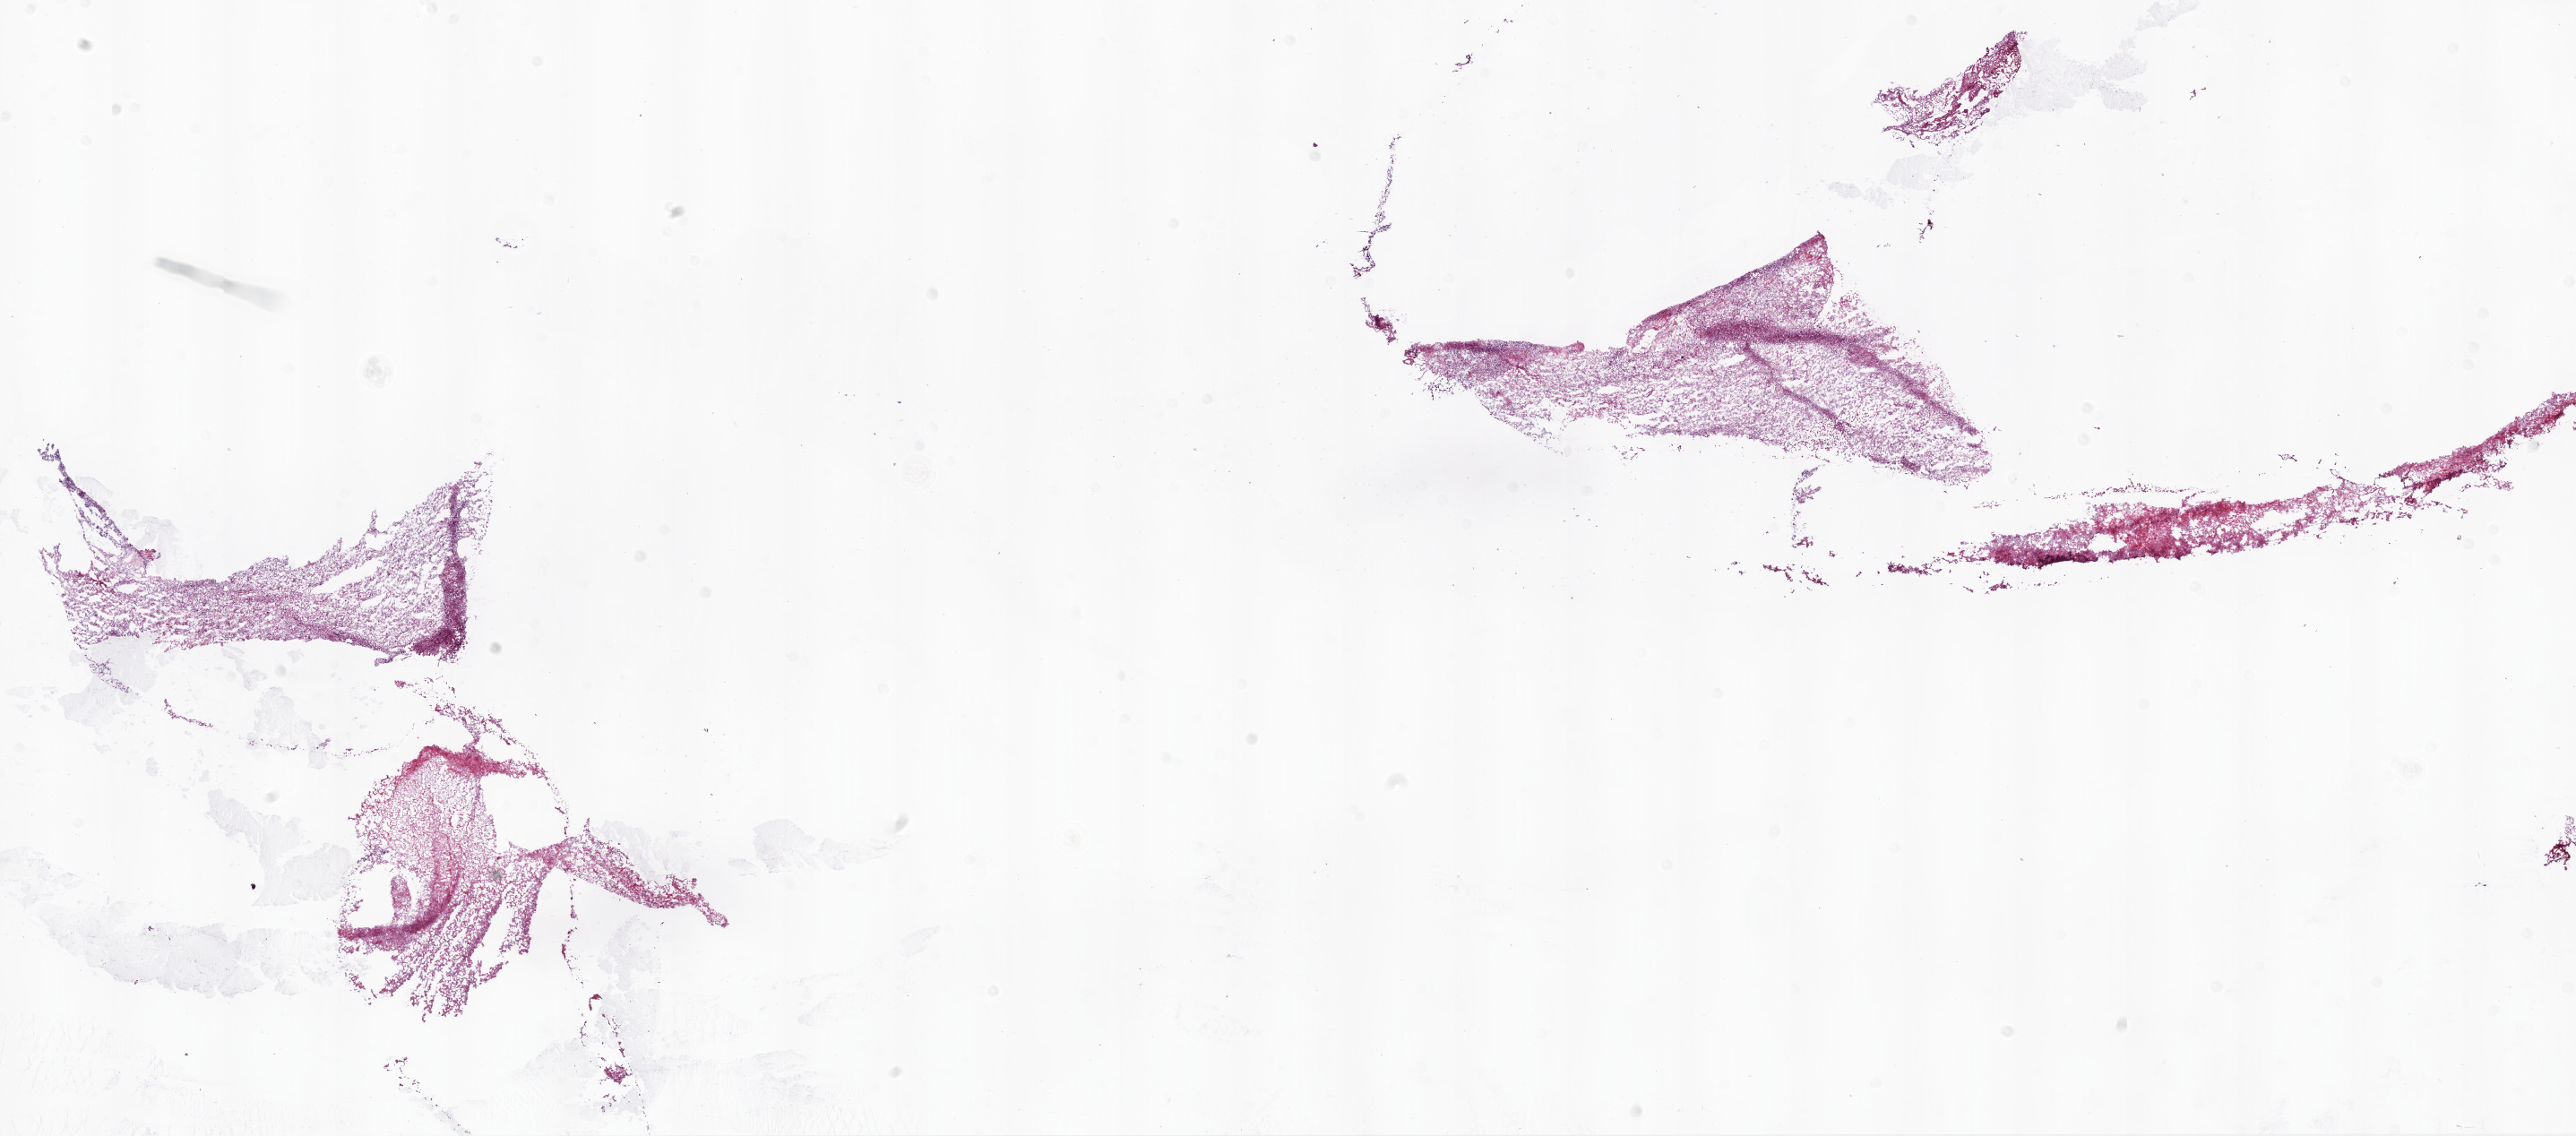
Whole-slide histology image, H&E-stained — a low-resolution overview of the entire scanned area, about 23.1 x 10.2 mm, frozen section from the bottom of the tissue portion, brain, primary tumour sample. Male, age 59 years at initial diagnosis. Composition of this section per pathologist review: tumour cells 95%, tumour nuclei 100%, normal cells 0%, stromal cells 0%, necrosis 5%.
Pathologic diagnosis: Glioblastoma.